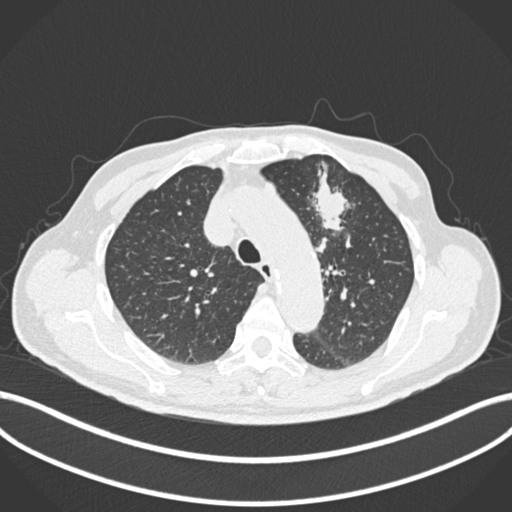
Chest CT, one axial slice. Slice 187 of 261 in the series (ordered by position). Reconstruction kernel B30f. 120 kVp. Lung window (W 1500 / L -600 HU). 1 mm slice thickness. 512 × 512 image matrix. Patient: male, 74 years. From the clinical record (not read from this slice): clinical TNM (as recorded): T2b N0 M1c.
Structures marked on this image (rectangle marked by the reading radiologist):
- lung tumour (recorded histology: adenocarcinoma): bounding box [x1, y1, x2, y2] px = [309, 166, 354, 239]